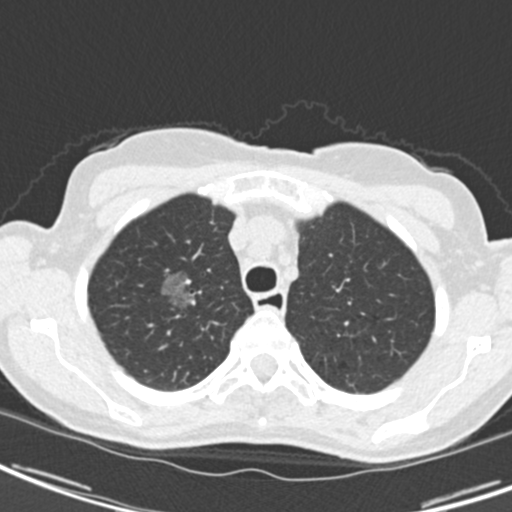
Low-dose screening chest CT, one axial slice. Position 160 of 189 along the scan axis. Reconstruction kernel B30f. 120 kVp. Lung window (W 1500 / L -600 HU). 2 mm slice thickness. 512 × 512 image matrix.
Annotated regions visible in this slice (expert manual segmentation):
- lesion 1 (tumor, upper lobe of right lung): box from (x=160, y=269) to (x=190, y=310) px